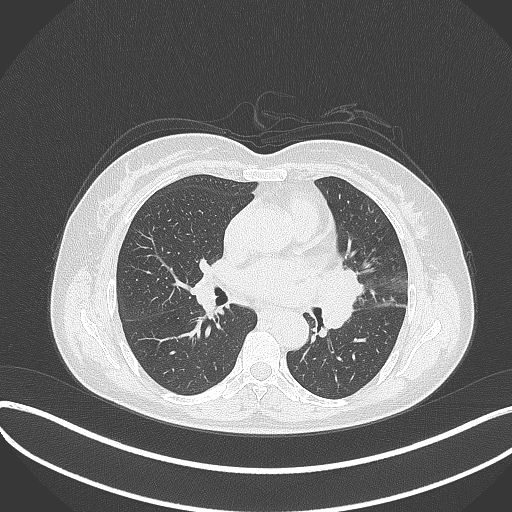
Chest CT, one axial slice. Position 185 of 373 along the scan axis. Reconstruction kernel B70f. 120 kVp. Lung window (W 1500 / L -600 HU). 1 mm slice thickness. 512 × 512 image matrix, field of view 400 × 400 mm. Patient: female, 54 years. Case-level facts recorded for this patient, not image findings: clinical TNM (as recorded): T2a N1 M0; histopathological grade: G3.
Outlined on this slice (rectangle marked by the reading radiologist):
- lung tumour (recorded histology: small cell carcinoma): box from (x=319, y=264) to (x=366, y=337) px